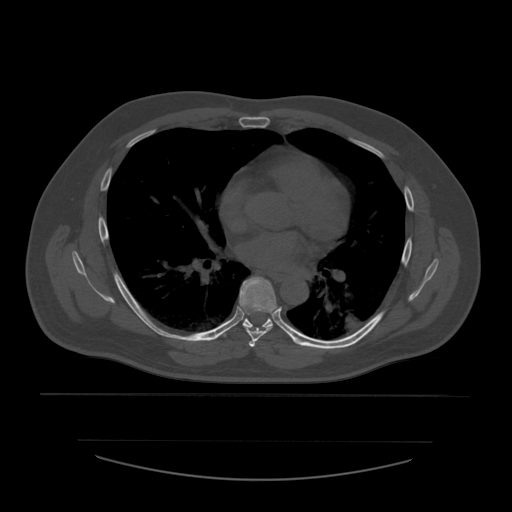
CT including the spine, one axial slice; slice 370 of 532 in the series (ordered by position); bone window (W 1800 / L 400 HU); 512 × 512 image matrix, field of view 441 × 441 mm. Patient age 44 years. From the clinical record (not read from this slice): primary cancer: soft tissue sarcoma.
Outlined on this slice (semi-automatically segmented with operator editing):
- T5 vertebra: bounding box <249,341,255,348> (left, top, right, bottom; pixels)
- T6 vertebra: <240,277,277,346>
- T7 vertebra: <216,319,291,339>